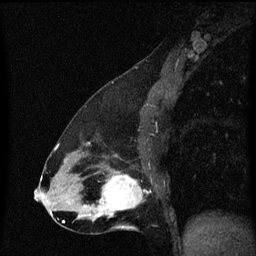
Breast MRI (dynamic contrast-enhanced), one sagittal slice; slice 31 of 60 in the series (ordered by position); dynamic contrast-enhanced series, image 2 of 3 at this slice position (ordered by acquisition); 1.5 T; TE 4.2 ms, TR 8.4 ms; 2 mm slice thickness; 256 × 256 image matrix. Patient: female, 47 years.
Annotated regions visible in this slice (semi-automatic segmentation, software-assisted and operator-edited):
- analysis volume of interest (the breast-tissue region the enhancement analysis was run in; not a lesion): box from (x=100, y=172) to (x=144, y=219) px
- tumour enhancement mask (voxels above the 70 % enhancement threshold inside the analysis volume of interest): (x=100, y=176)–(x=143, y=217)